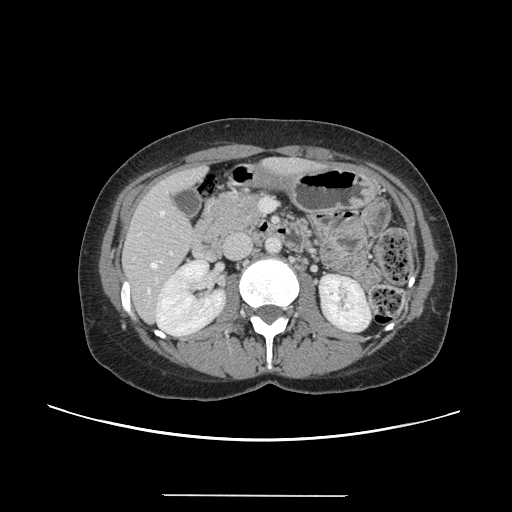
Contrast-enhanced abdominal CT, one axial slice. Slice 57 of 144 in the series (ordered by position). 120 kVp. Intravenous contrast given. Soft-tissue window (W 400 / L 40 HU). 2.5 mm slice thickness. 512 × 512 image matrix, field of view 380 × 380 mm. Female patient, age 53 years. From the clinical record (not read from this slice): diagnosis: colorectal cancer liver metastases, imaged before liver resection; multiple liver metastases: yes.
Structures marked on this image (expert manual segmentation):
- hepatic veins: bounding box (x1, y1, x2, y2) in pixels: (148, 211, 164, 293)
- liver: (124, 159, 318, 319)
- planned liver remnant (the part of the liver to remain after resection): (124, 159, 320, 311)
- portal vein (with intrahepatic branches): (155, 252, 173, 282)